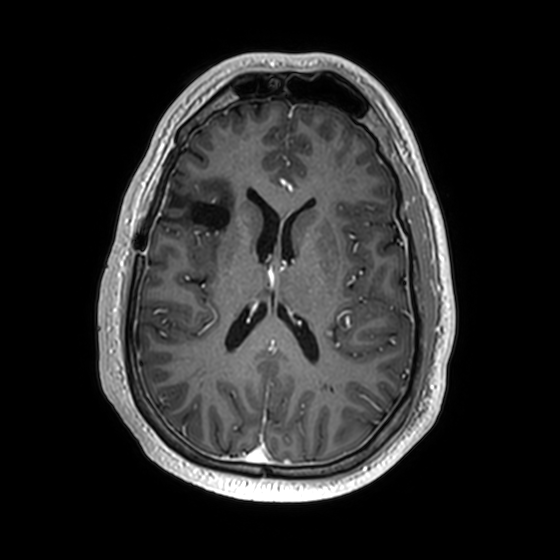
Brain MRI from a brain-tumour surgery series, one axial slice; slice 78 of 174 in the series (ordered by position); T1-weighted post-contrast; 1 mm slice thickness; 560 × 560 image matrix, field of view 256 × 256 mm. From the clinical record (not read from this slice): histopathology: Astrocytoma; WHO grade: 2; IDH mutation: yes.
Annotated regions visible in this slice (expert manual segmentation):
- previous resection cavity: bounding box (x1, y1, x2, y2) in pixels: (159, 196, 229, 231)